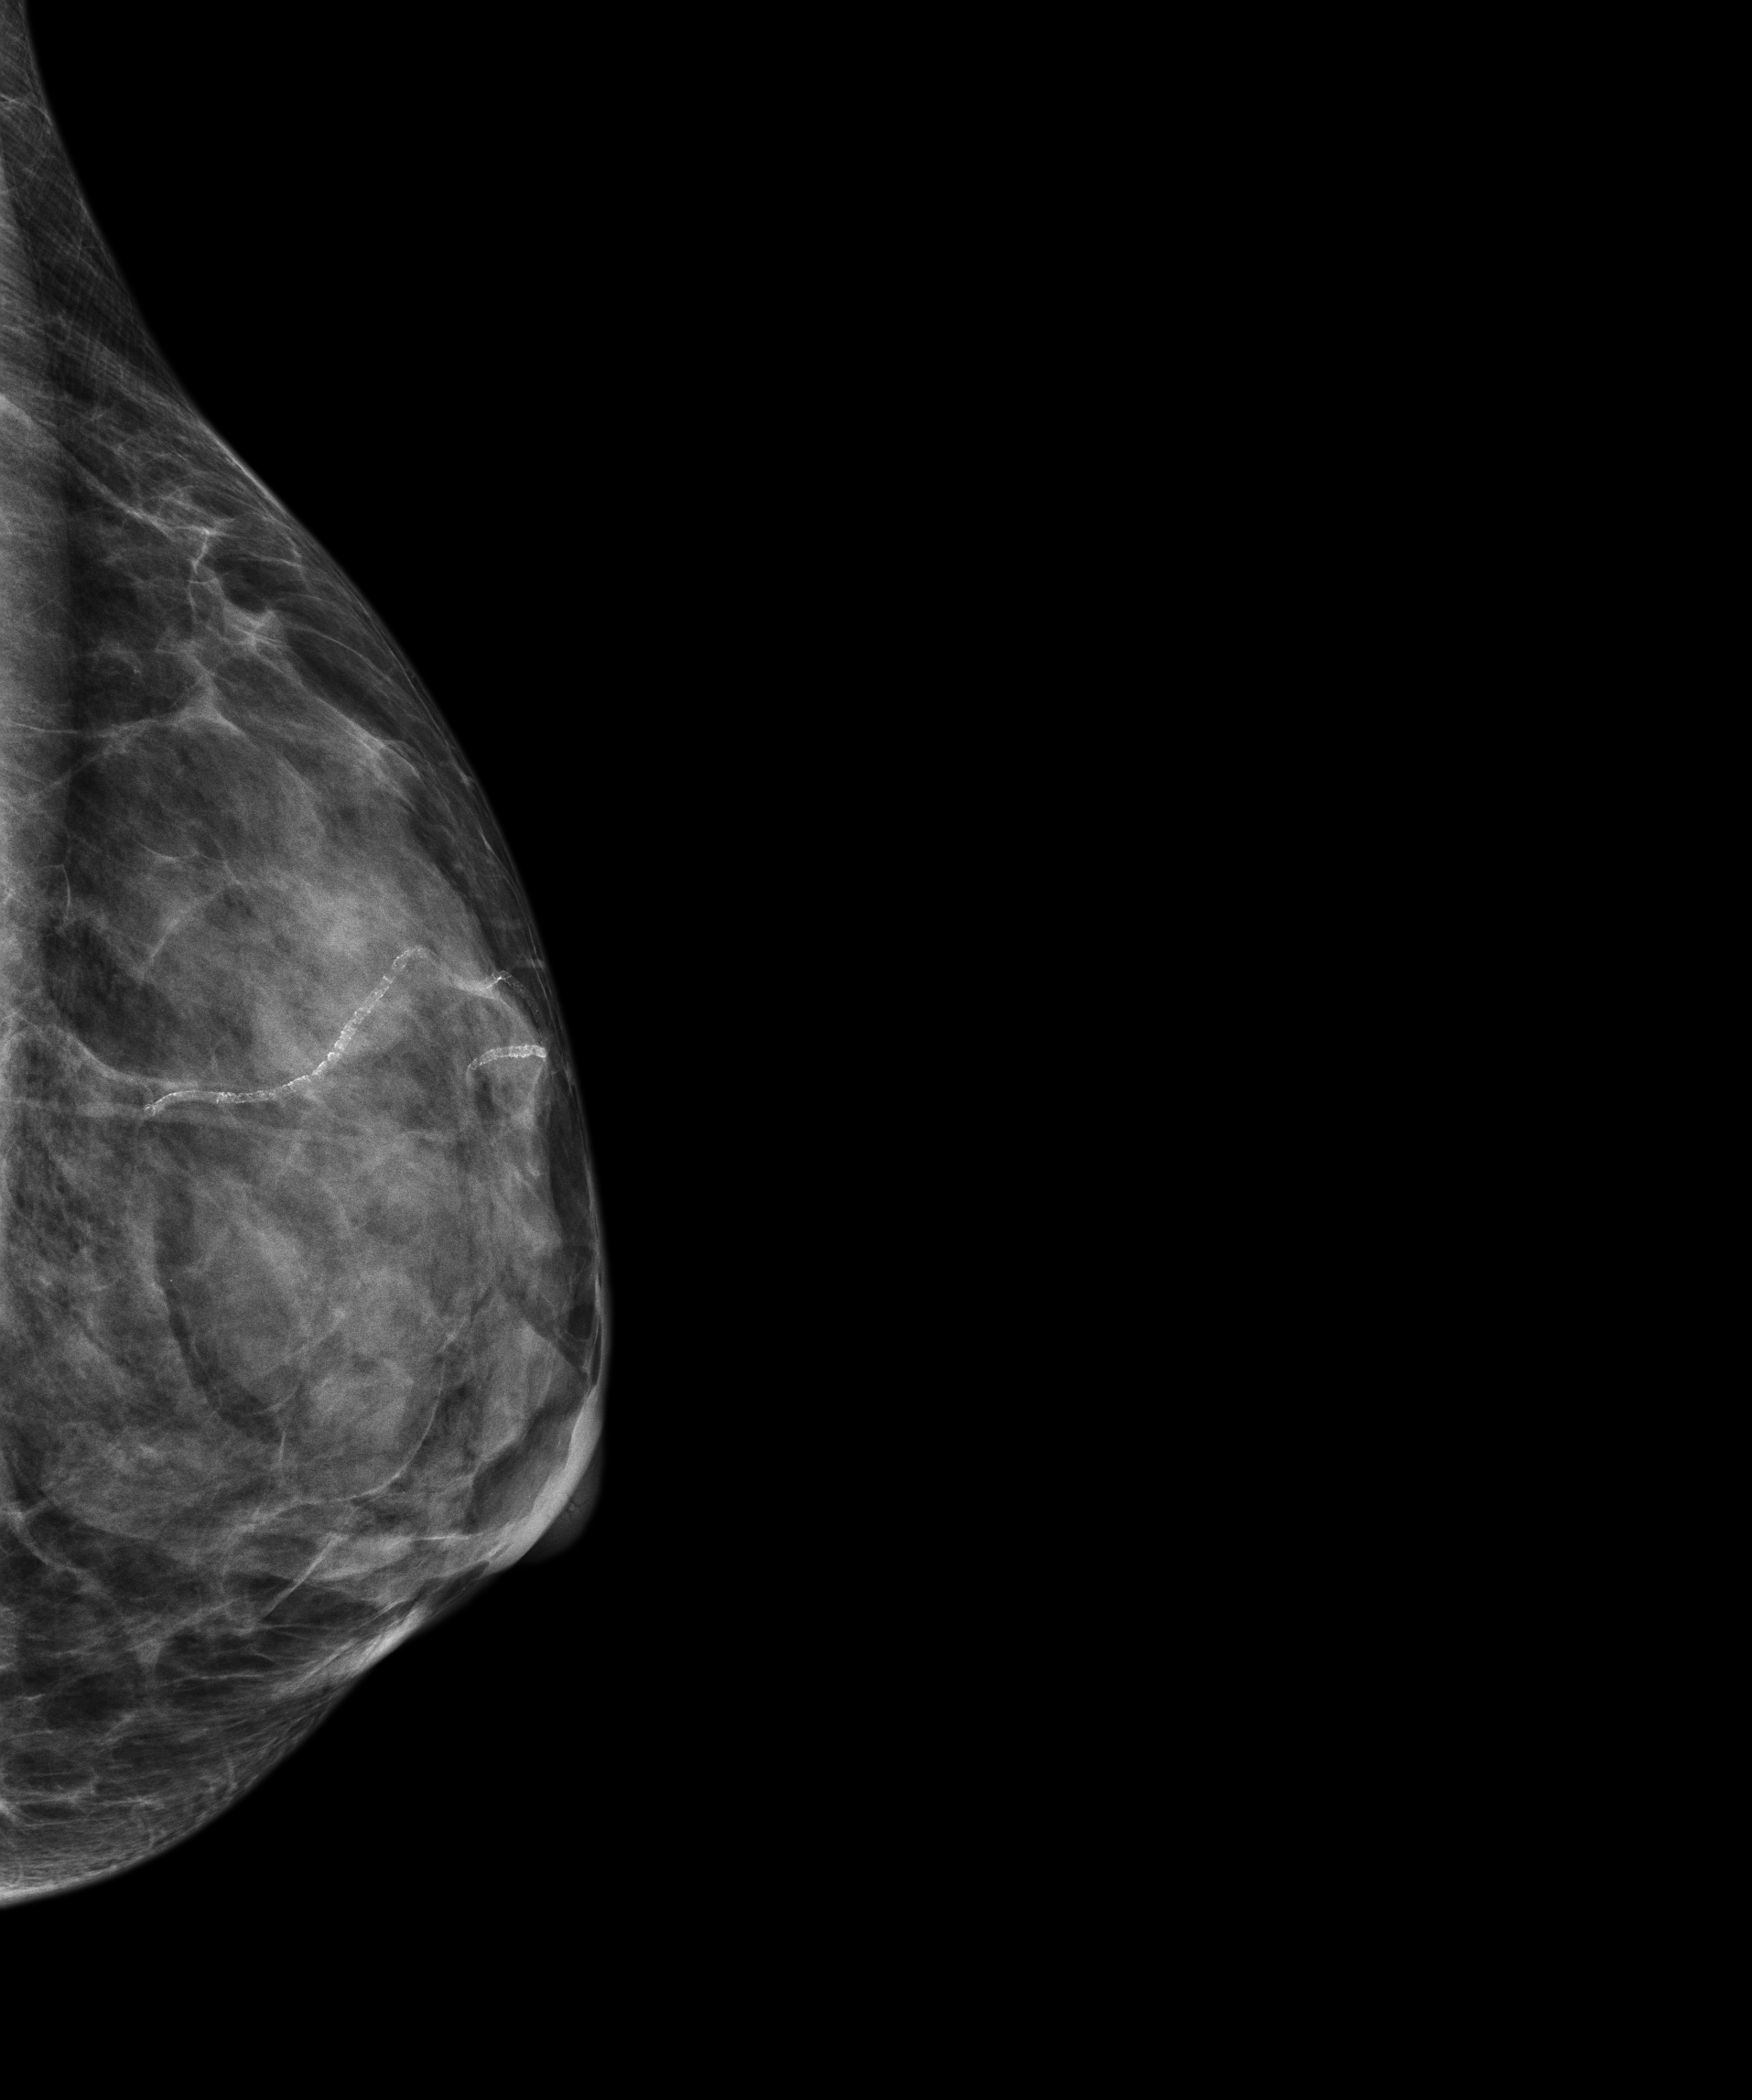
Digital mammogram (FFDM); left breast; exaggerated CC view (lateral); screening examination; compressed breast thickness 31 mm; system: Senographe Essential ADS_56.21.3. Female patient, age 59 years.
- BI-RADS breast density category at the screening exam (both breasts, scale 1–4): 4
- final BI-RADS assessment for this screening round (tomosynthesis exam, both breasts): category 1
- recall: no recall after this screen